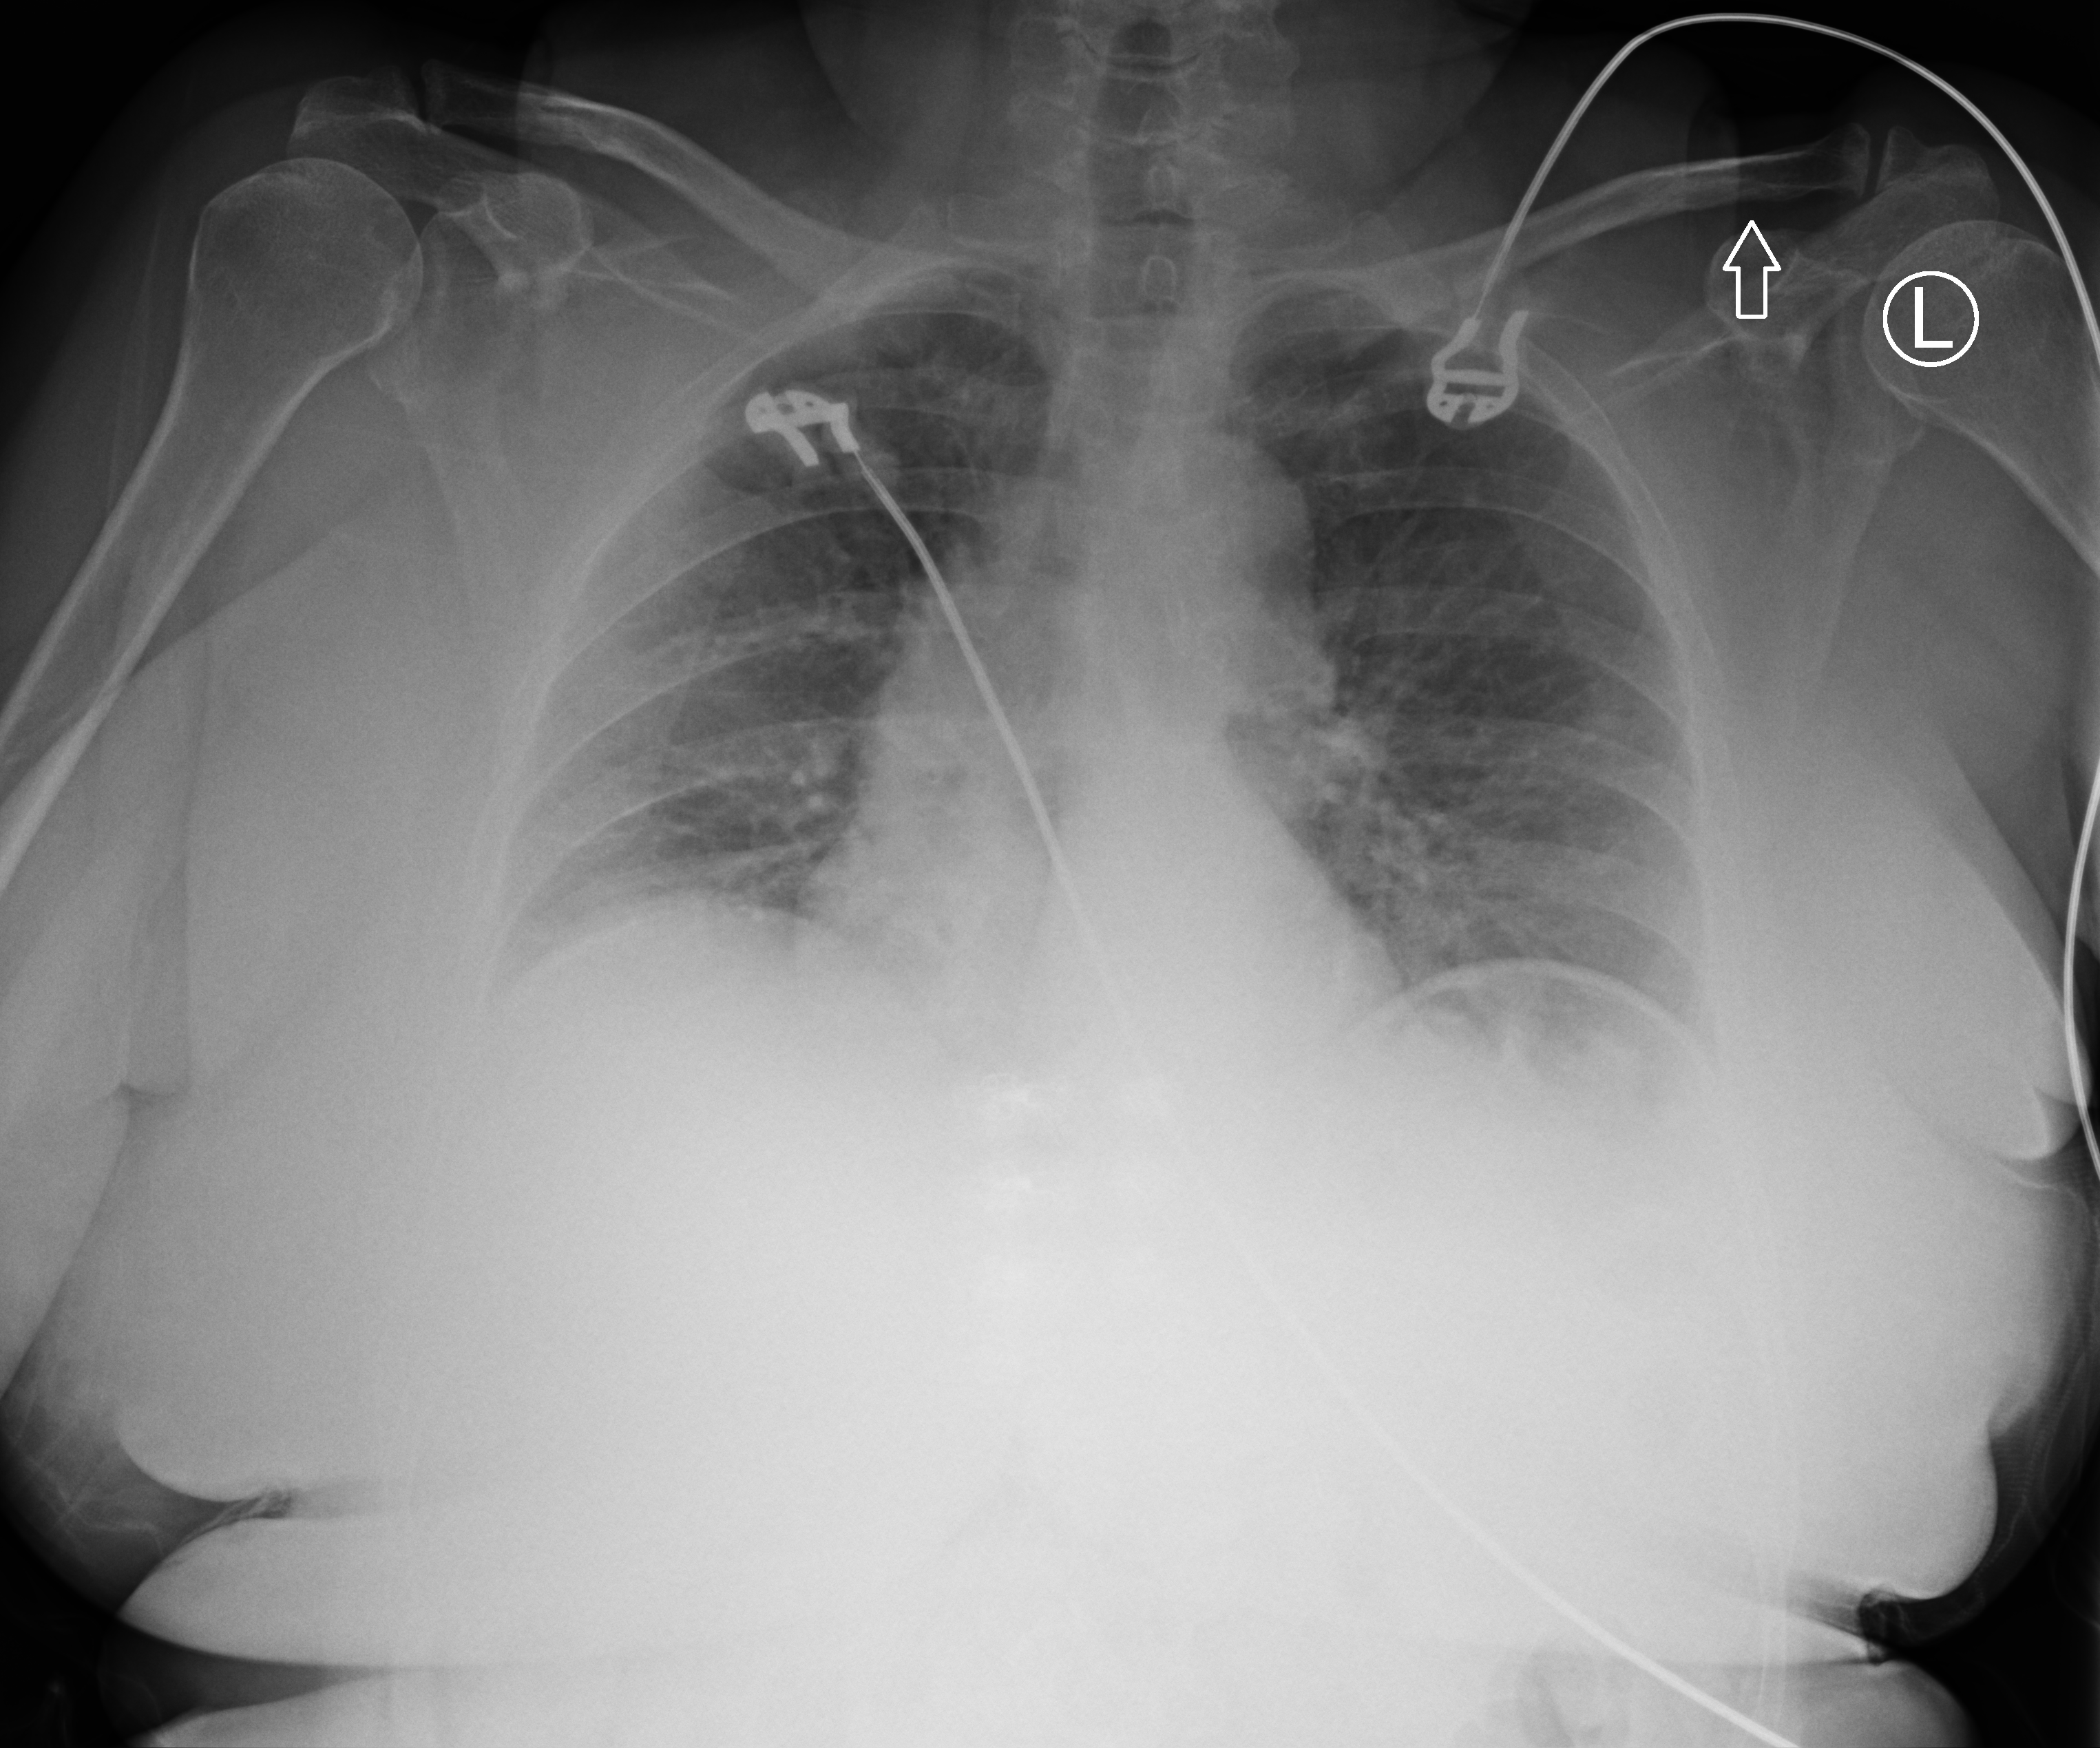
Chest X-ray (portable), anteroposterior (AP) projection. Female patient hospitalised with COVID-19, age 60–74 years.
Hospital-stay facts (about this admission, not read from this image; timing relative to this image not recorded):
- admitted to intensive care during this hospital stay: no